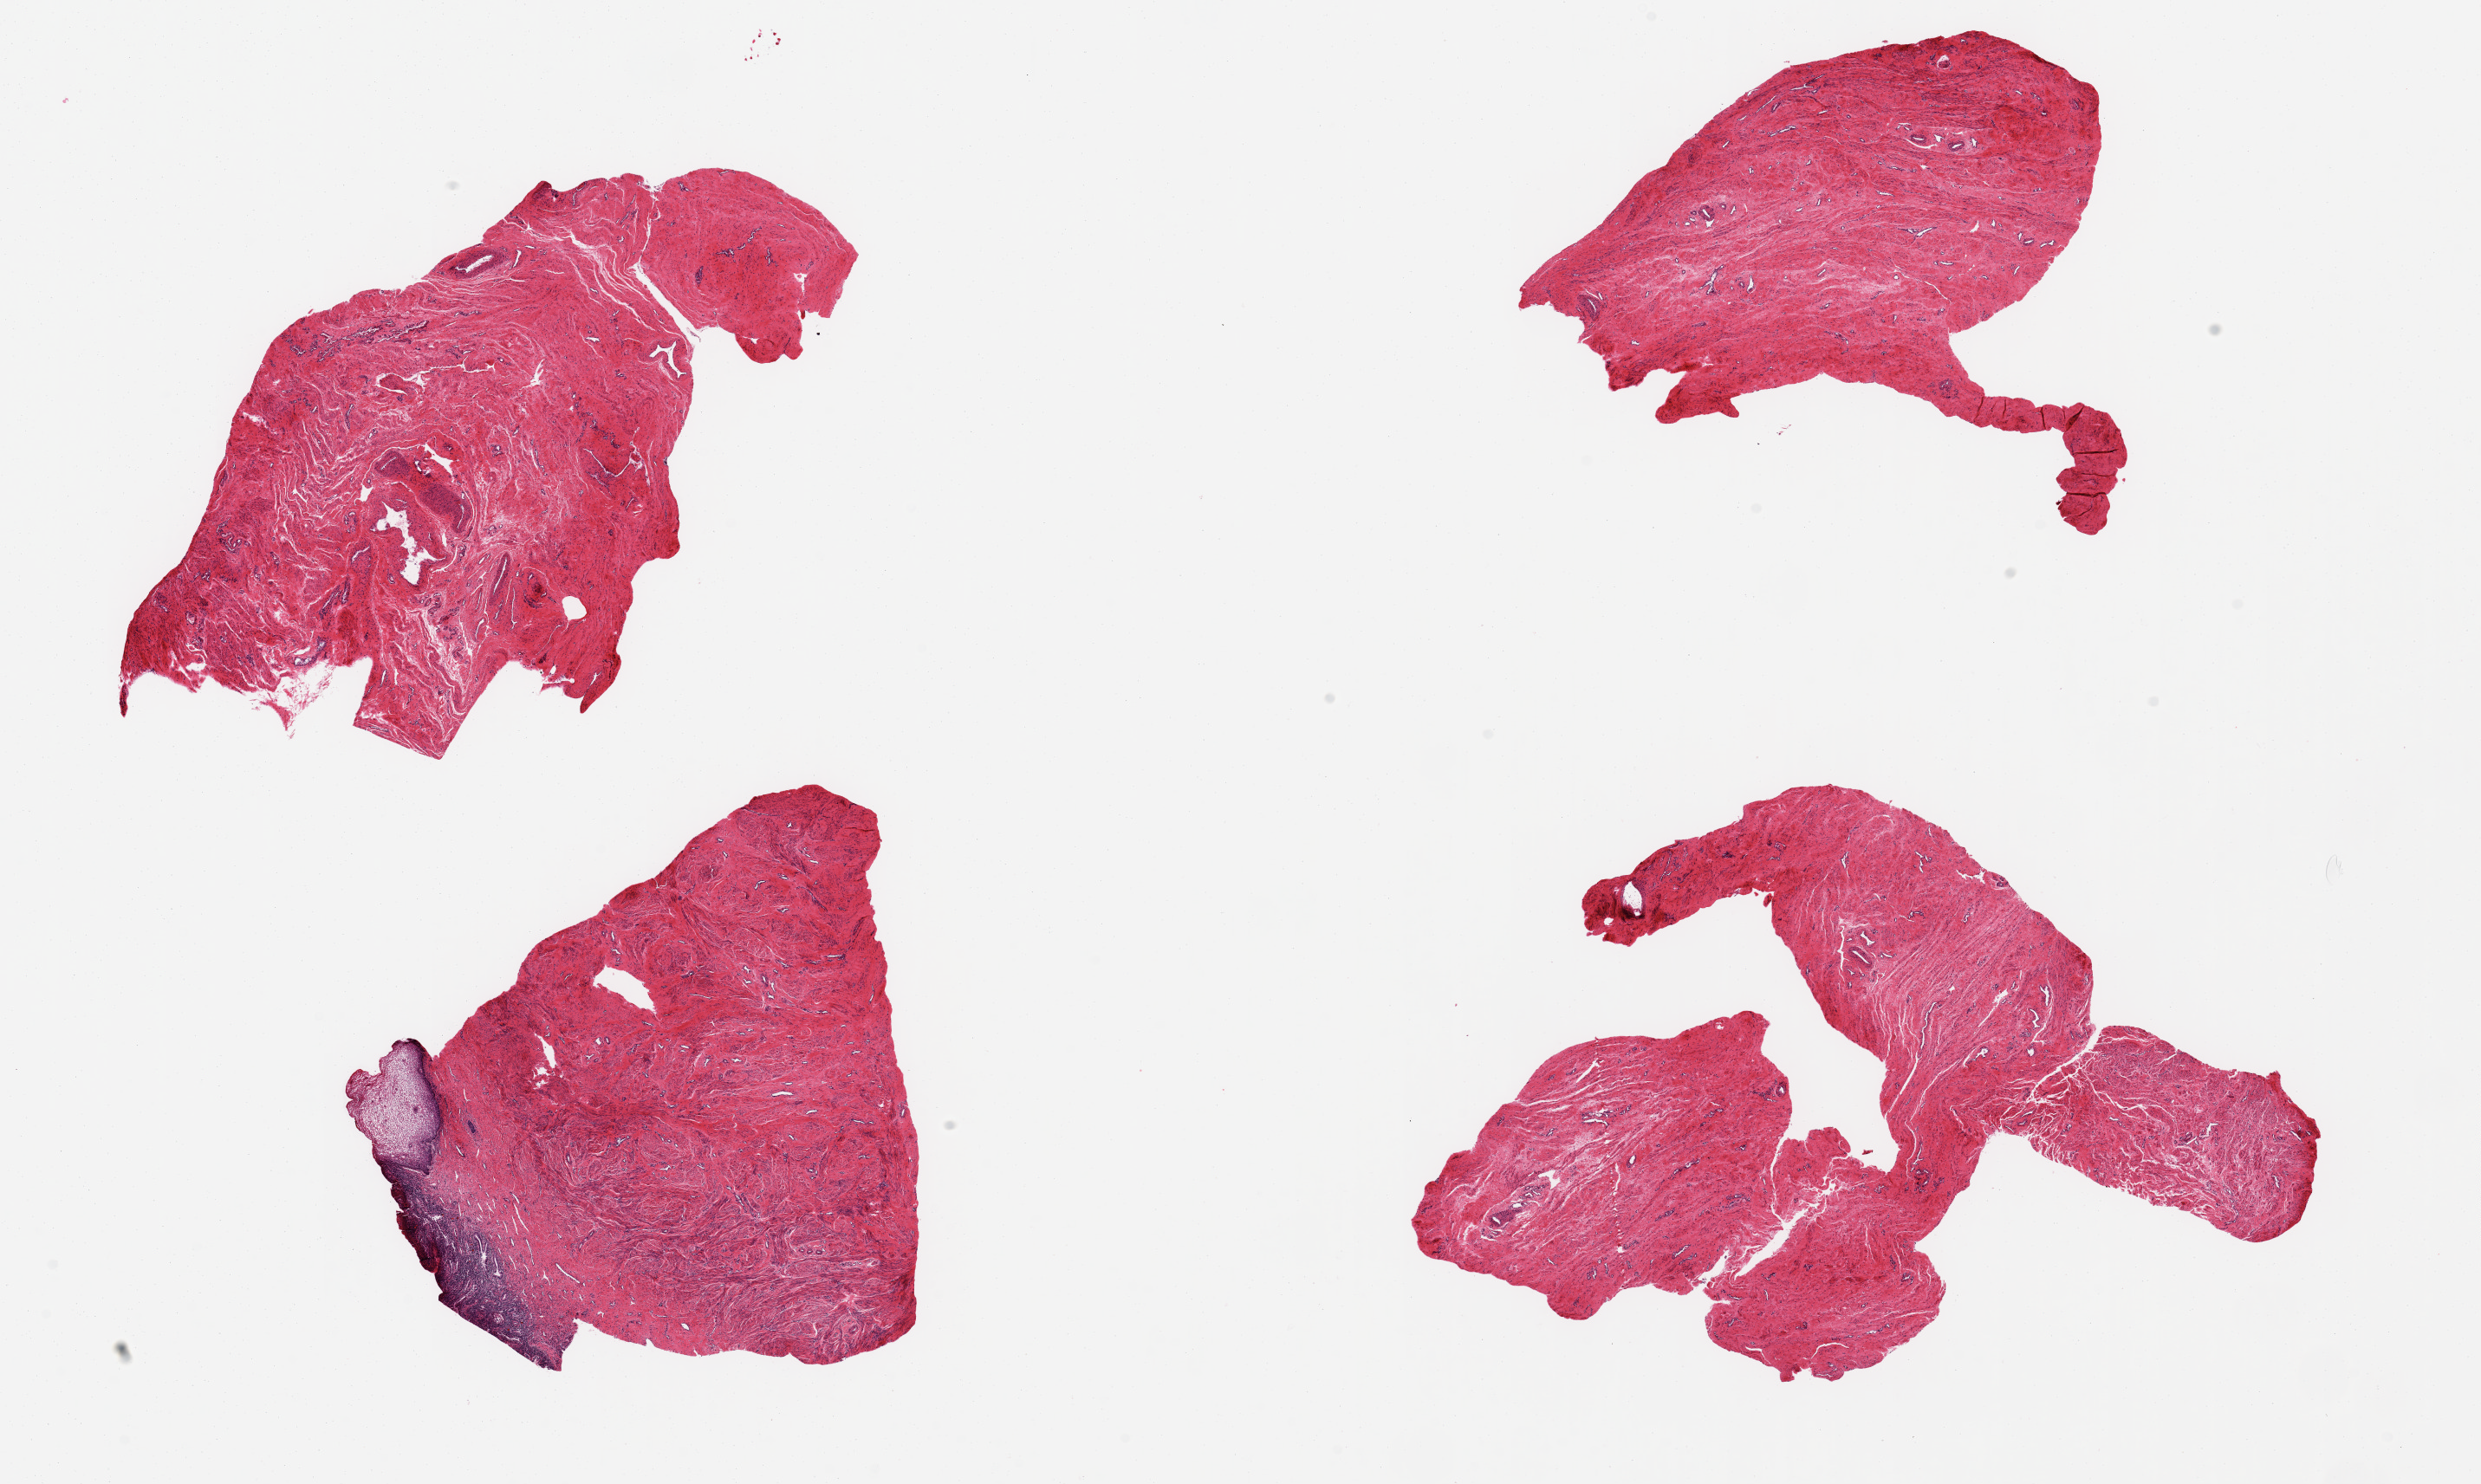
Digitized hematoxylin and eosin (H&E)-stained section — a low-resolution overview of the entire scanned area, about 22.6 x 13.5 mm; PAXgene-fixed paraffin-embedded (PFPE) section; sampled site (target tissue): endocervix; donor tissue sample.
Review note (as recorded): 4 pieces up to 5x5 mm; 1 piece has both squamous and glandular mucosa; others are without epithelium.